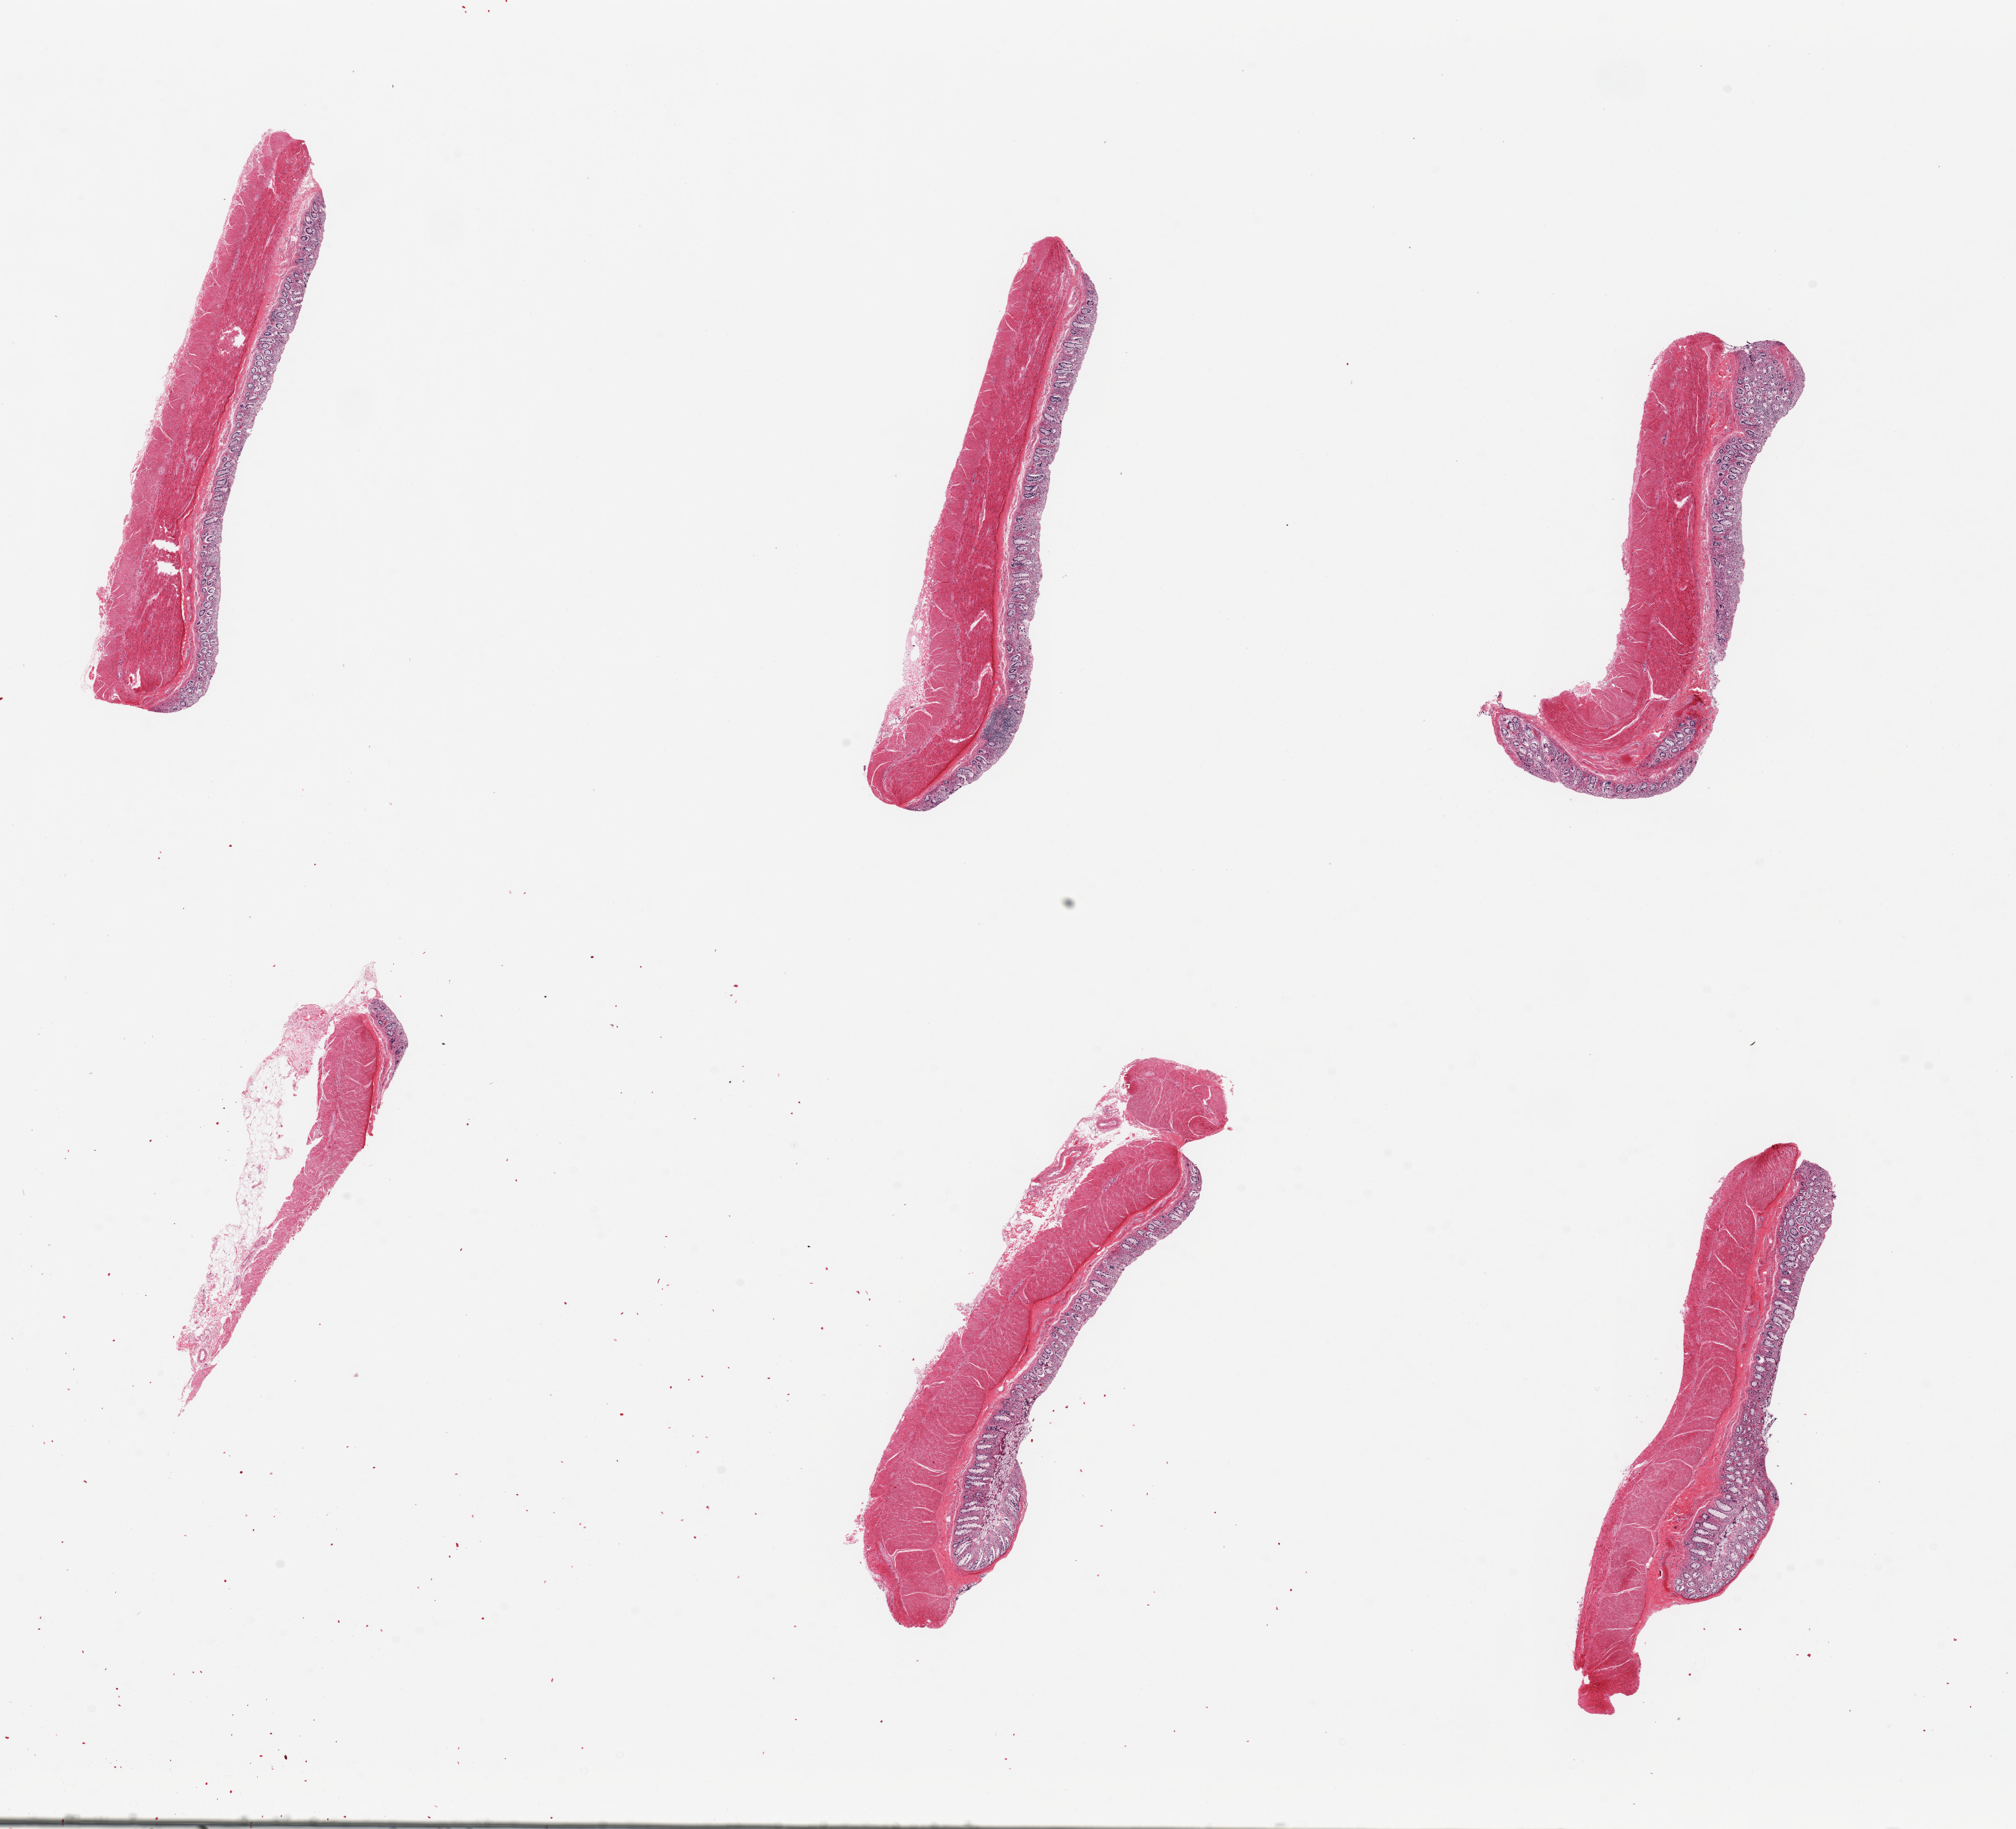
Whole-slide image, H&E stain, brightfield, low-resolution overview of the scanned area, about 24.6 x 22.3 mm, PAXgene-fixed, paraffin-embedded tissue, sampled site (target tissue): sigmoid colon, tissue donor sample. Male donor.
- pathologist's review note for this sample: 6 pieces ~7x 1.5mm Mucosa poorly preserved, ~30% of thickness (~300 microns)